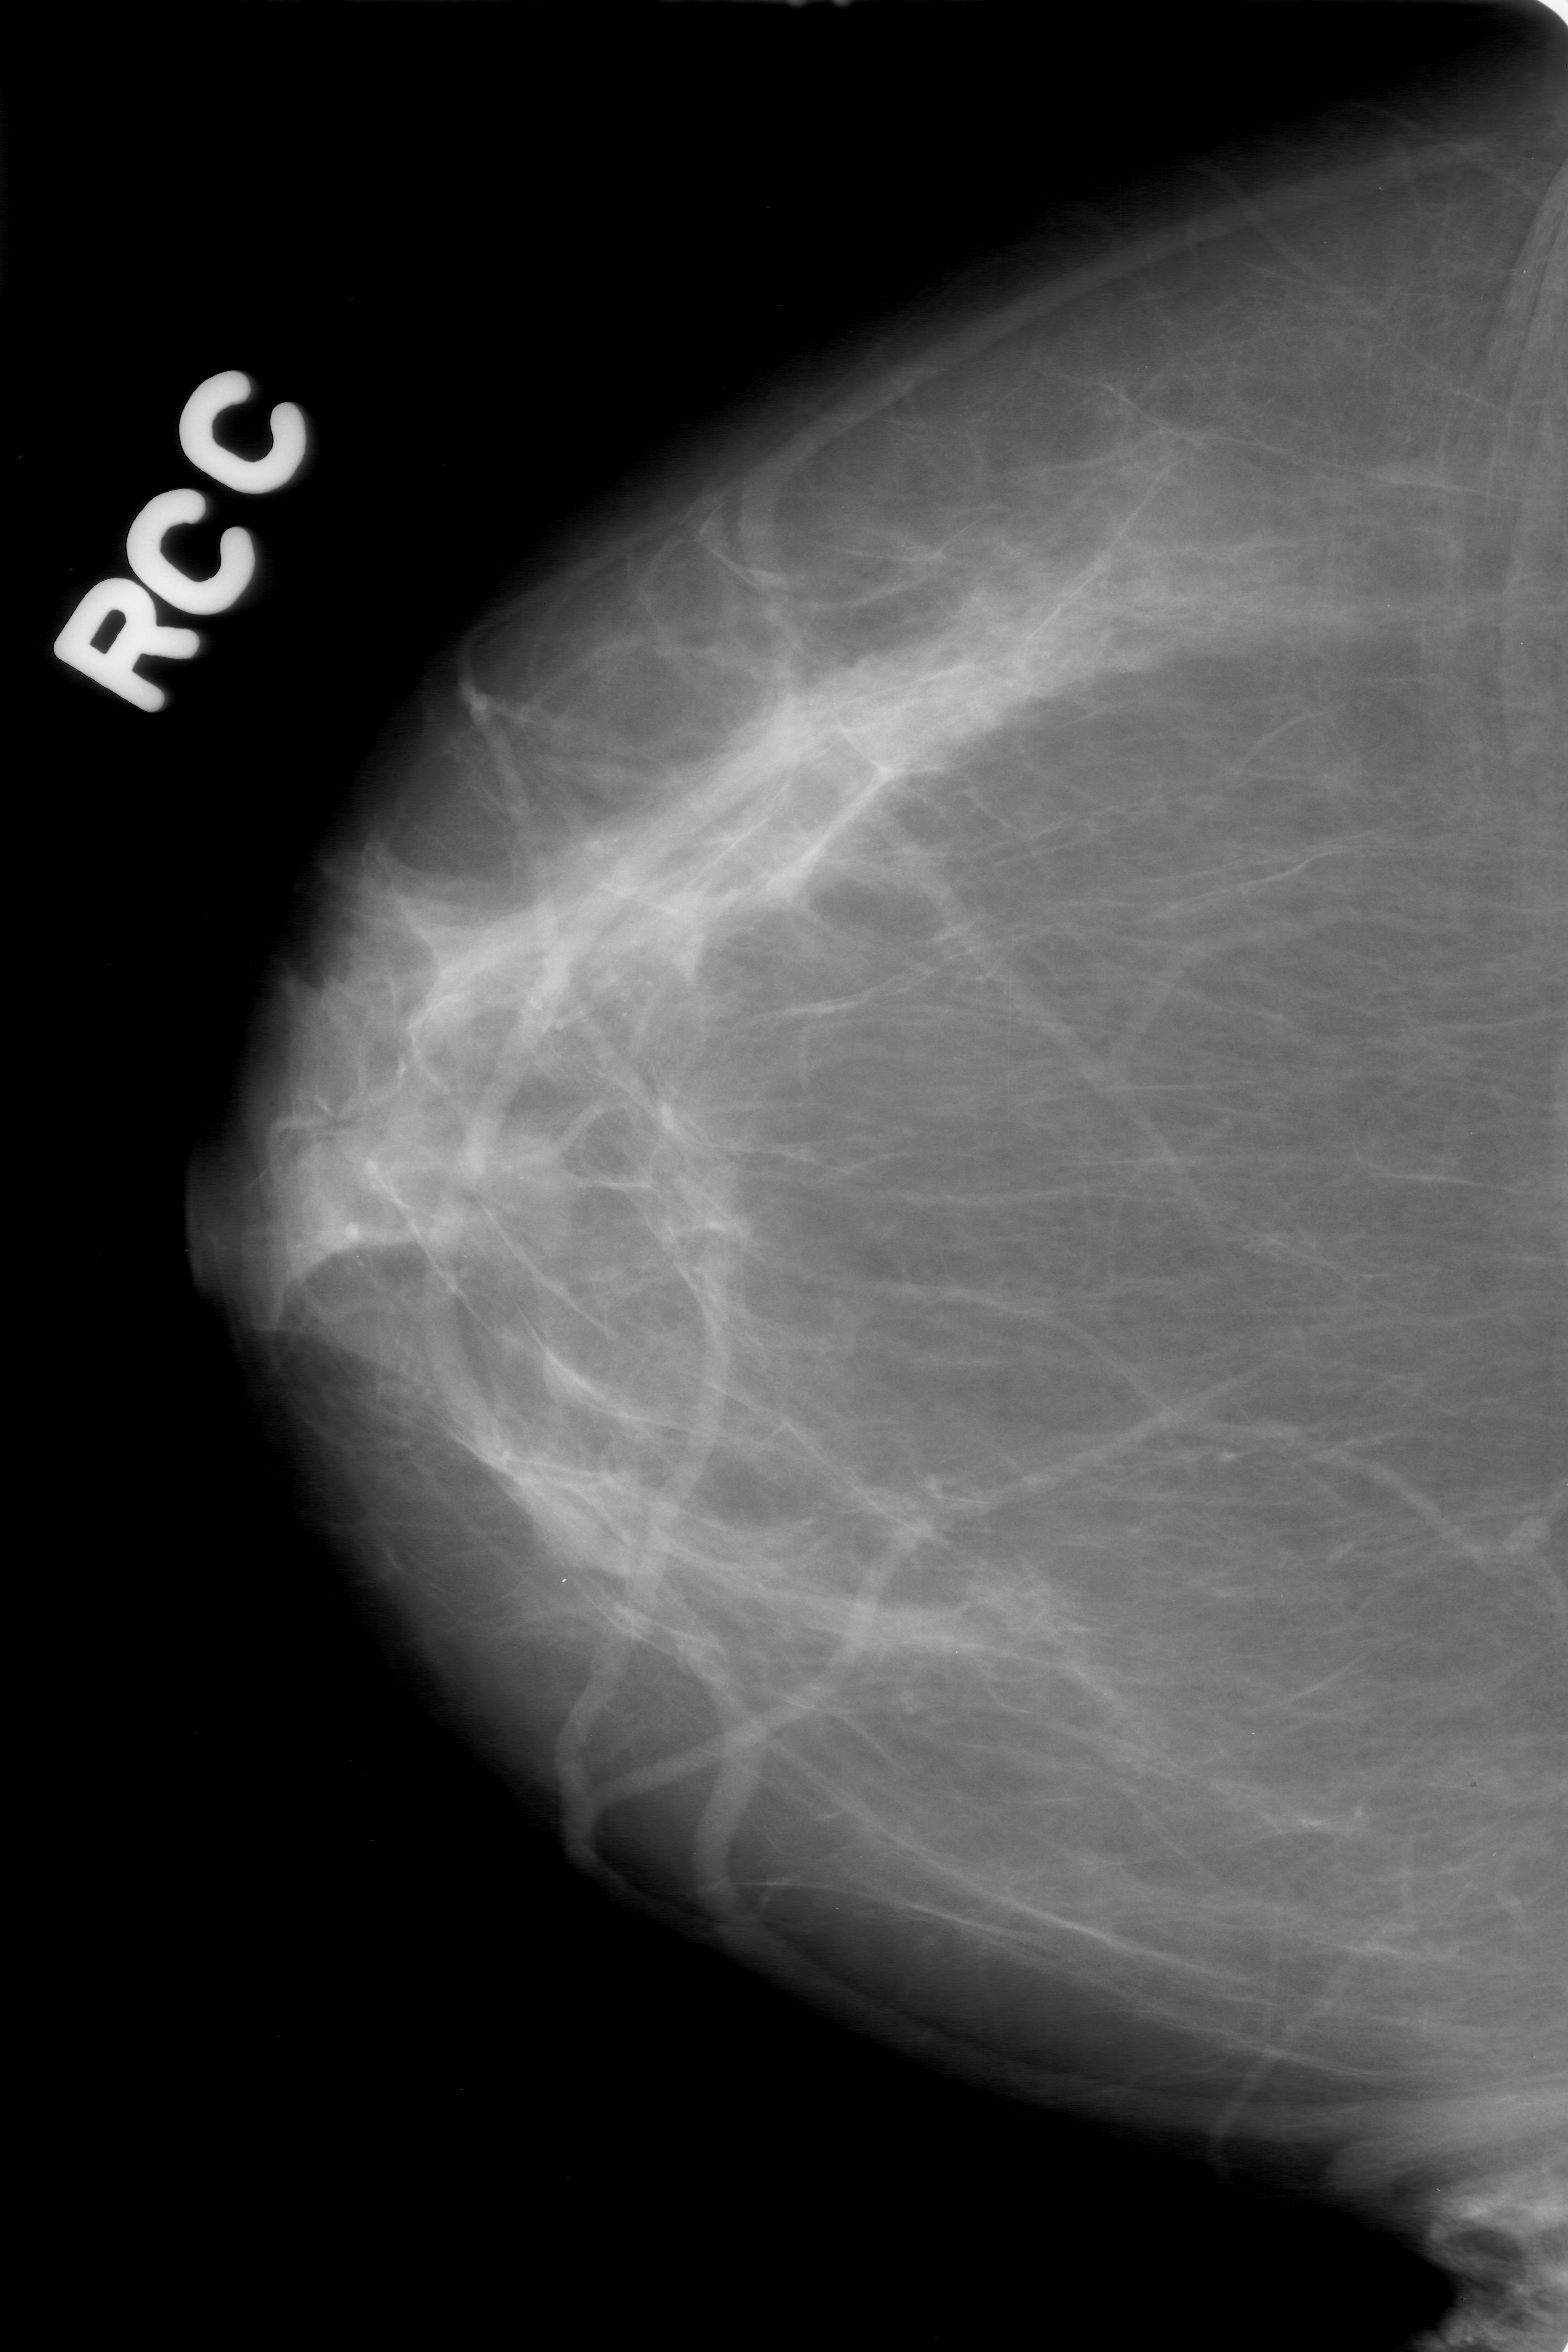
Mammogram (digitized film), right breast, craniocaudal (CC) view, breast composition: scattered fibroglandular densities (BI-RADS density category 2 of 4).
- Radiologist-marked abnormalities on this image: calcifications, morphology amorphous, distribution segmental; BI-RADS assessment category 0; pathology (as recorded): malignant.